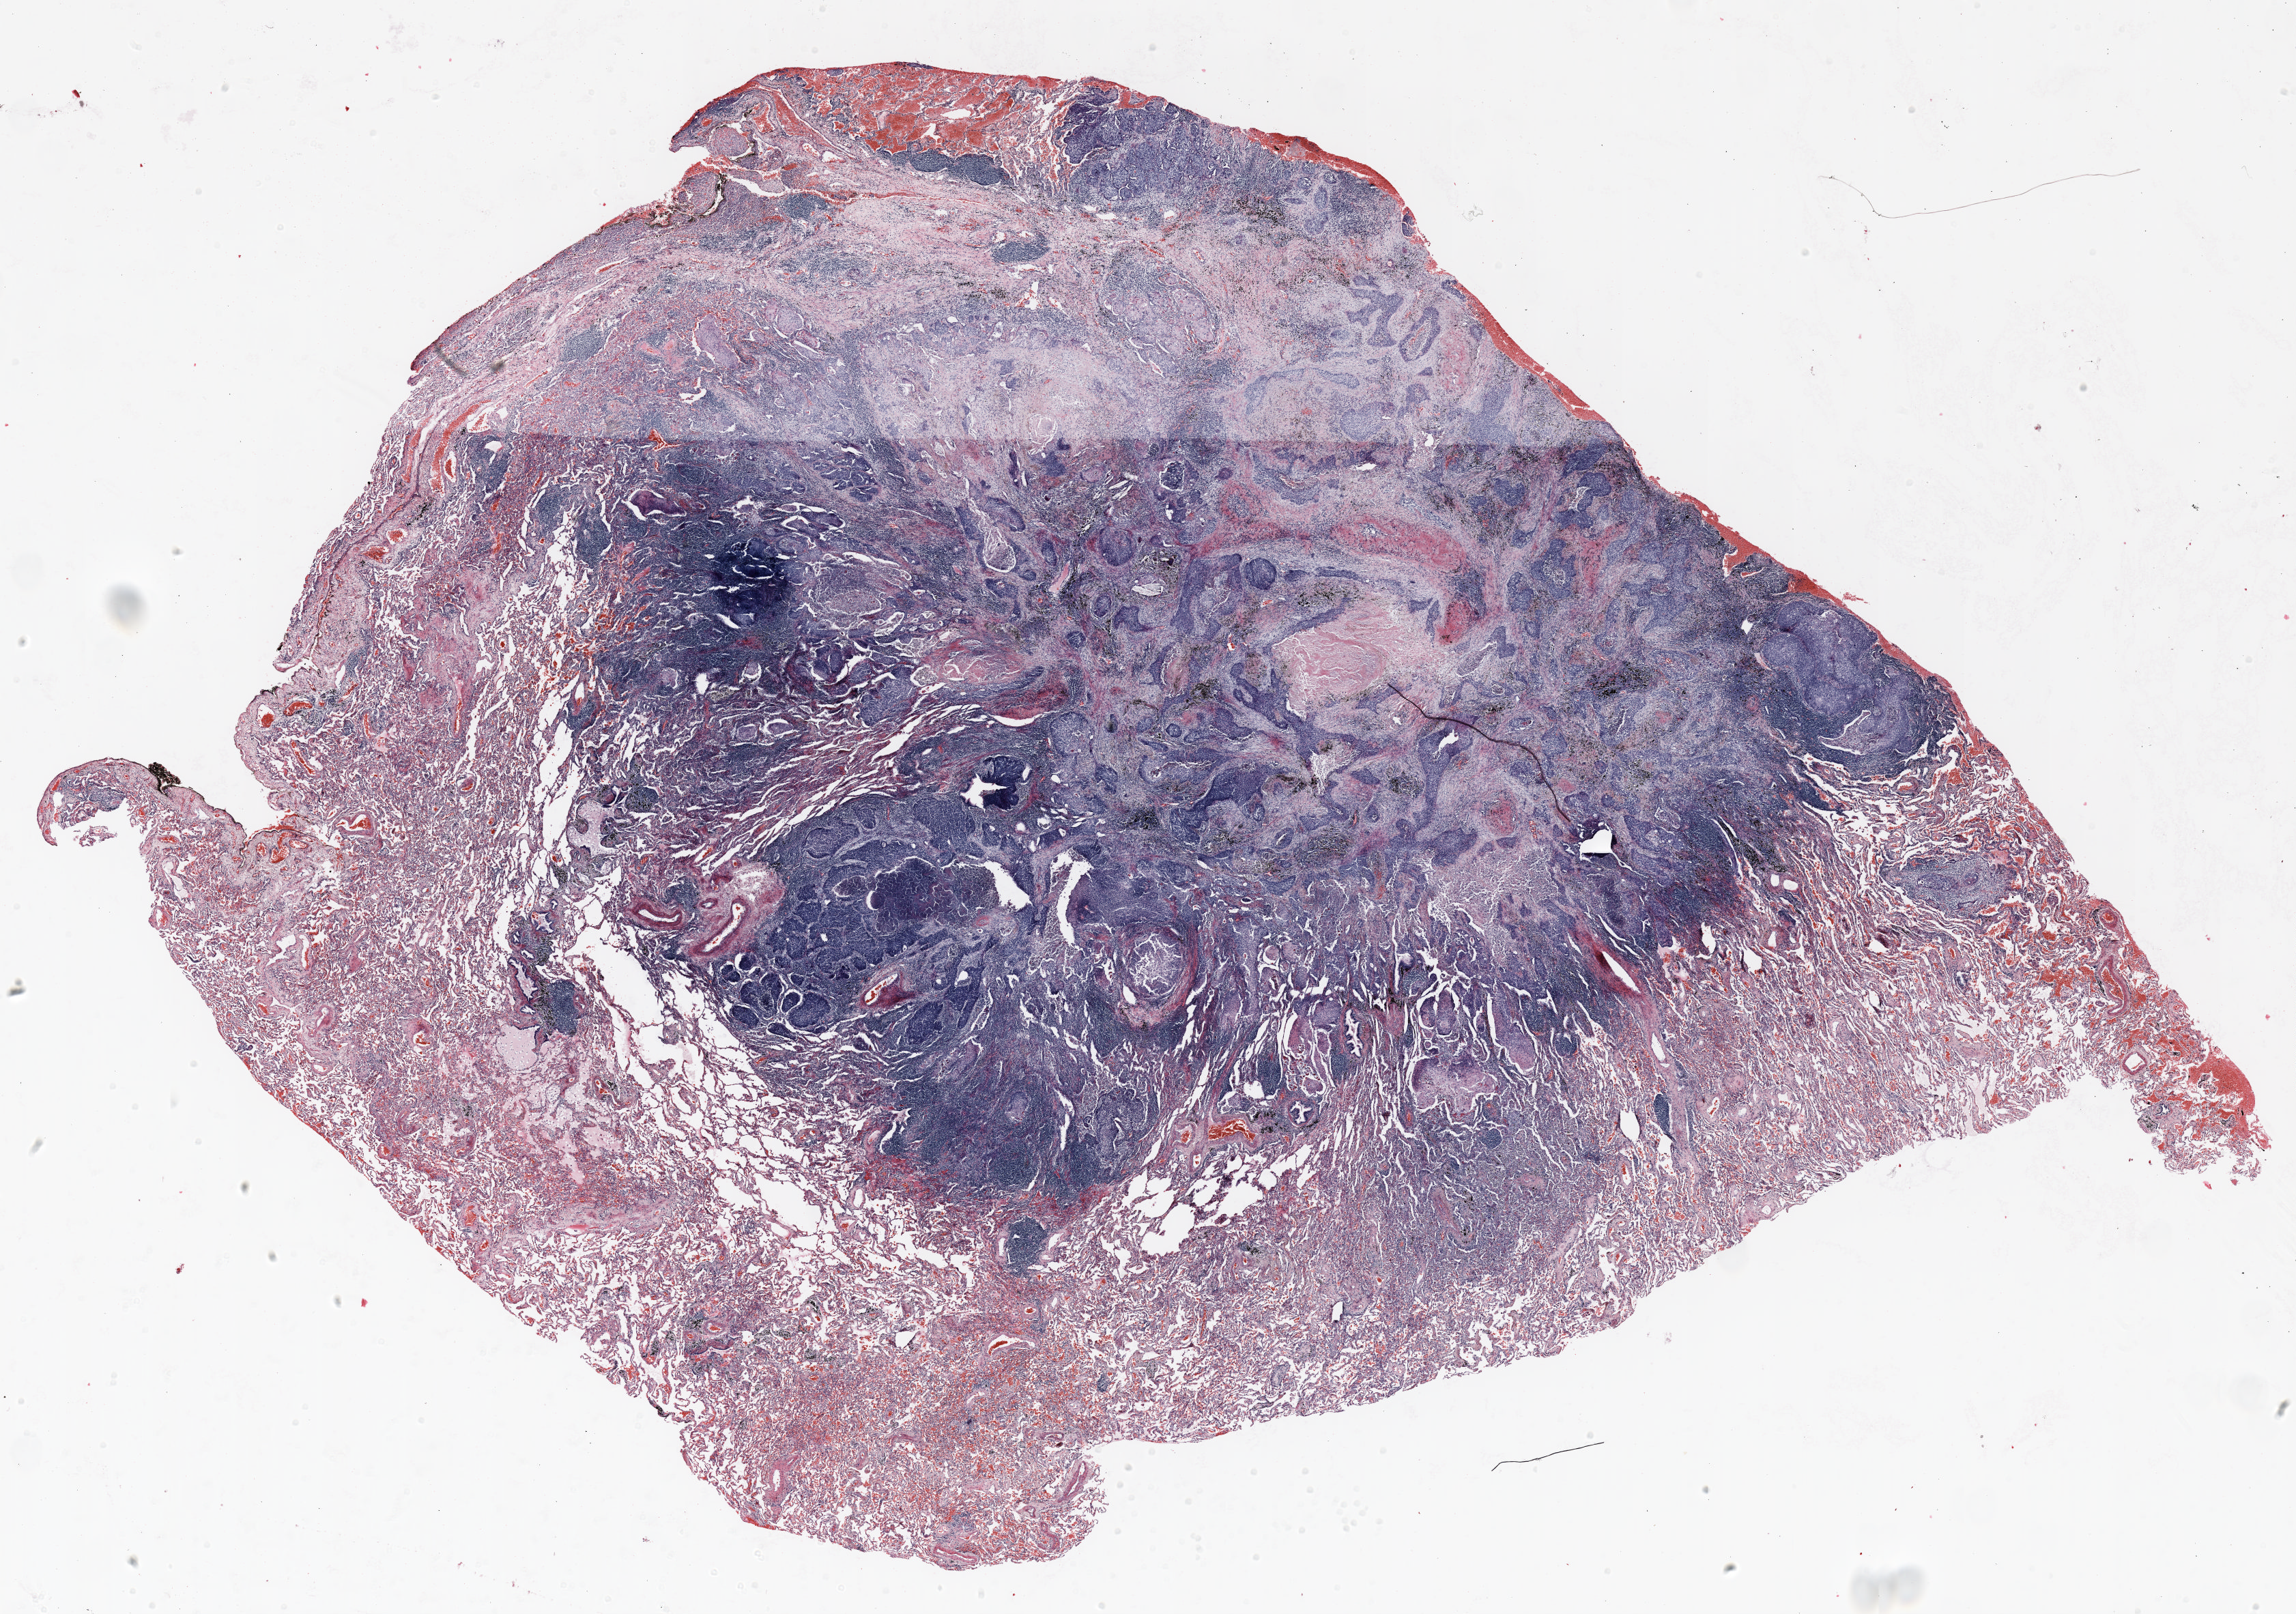
Hematoxylin and eosin (H&E) stained whole-slide image — whole scanned area (about 27.0 x 19.0 mm, slide scanned at 20x) shown as a low-resolution overview. FFPE section. Lung tissue. Male patient, aged 59 at enrolment.
Participant's lung-cancer diagnosis: Squamous cell carcinoma, NOS.